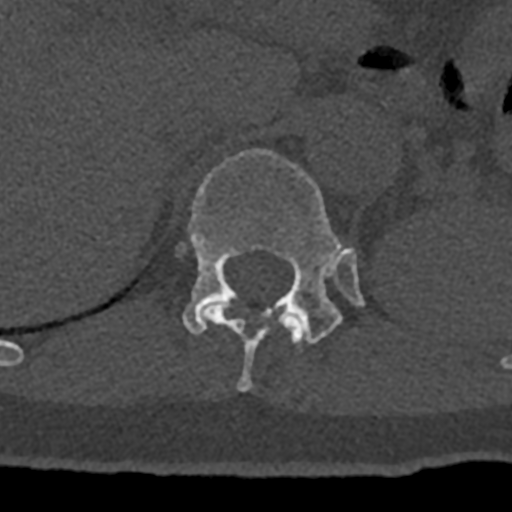
CT including the spine, one axial slice. Slice 511 of 797 in the series (ordered by position). Reconstruction kernel Br40s/3. 120 kVp. Bone window (W 1800 / L 400 HU). 0.5 mm slice thickness. 512 × 512 image matrix, field of view 160 × 160 mm. Male patient, age 74 years. Case-level facts recorded for this patient, not image findings: primary cancer: renal.
Structures marked on this image (semi-automatic segmentation, software-assisted and operator-edited):
- T11 vertebra: bounding box (x1, y1, x2, y2) in pixels: (202, 301, 304, 392)
- T12 vertebra: (179, 149, 364, 344)